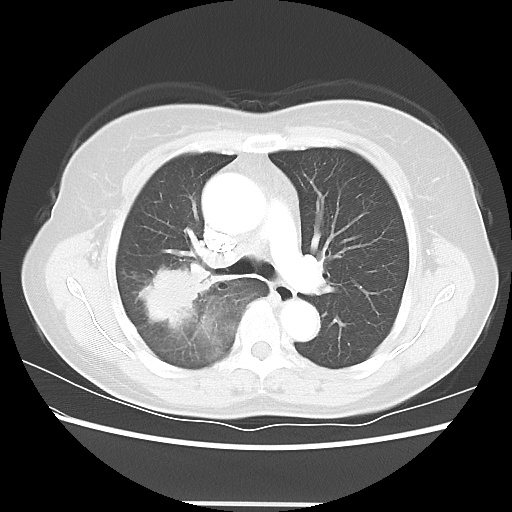
Chest CT, one axial slice; position 38 of 56 along the scan axis; 120 kVp; lung window (W 1500 / L -600 HU); 5 mm slice thickness; 512 × 512 image matrix, field of view 360 × 360 mm. Patient: female, 55 years. From the clinical record (not read from this slice): clinical TNM (as recorded): T2 N1 M0; histopathological grade: G2-3.
Outlined on this slice (bounding box drawn by a radiologist):
- lung tumour (recorded histology: adenocarcinoma): bounding box (x1, y1, x2, y2) in pixels: (137, 265, 224, 334)